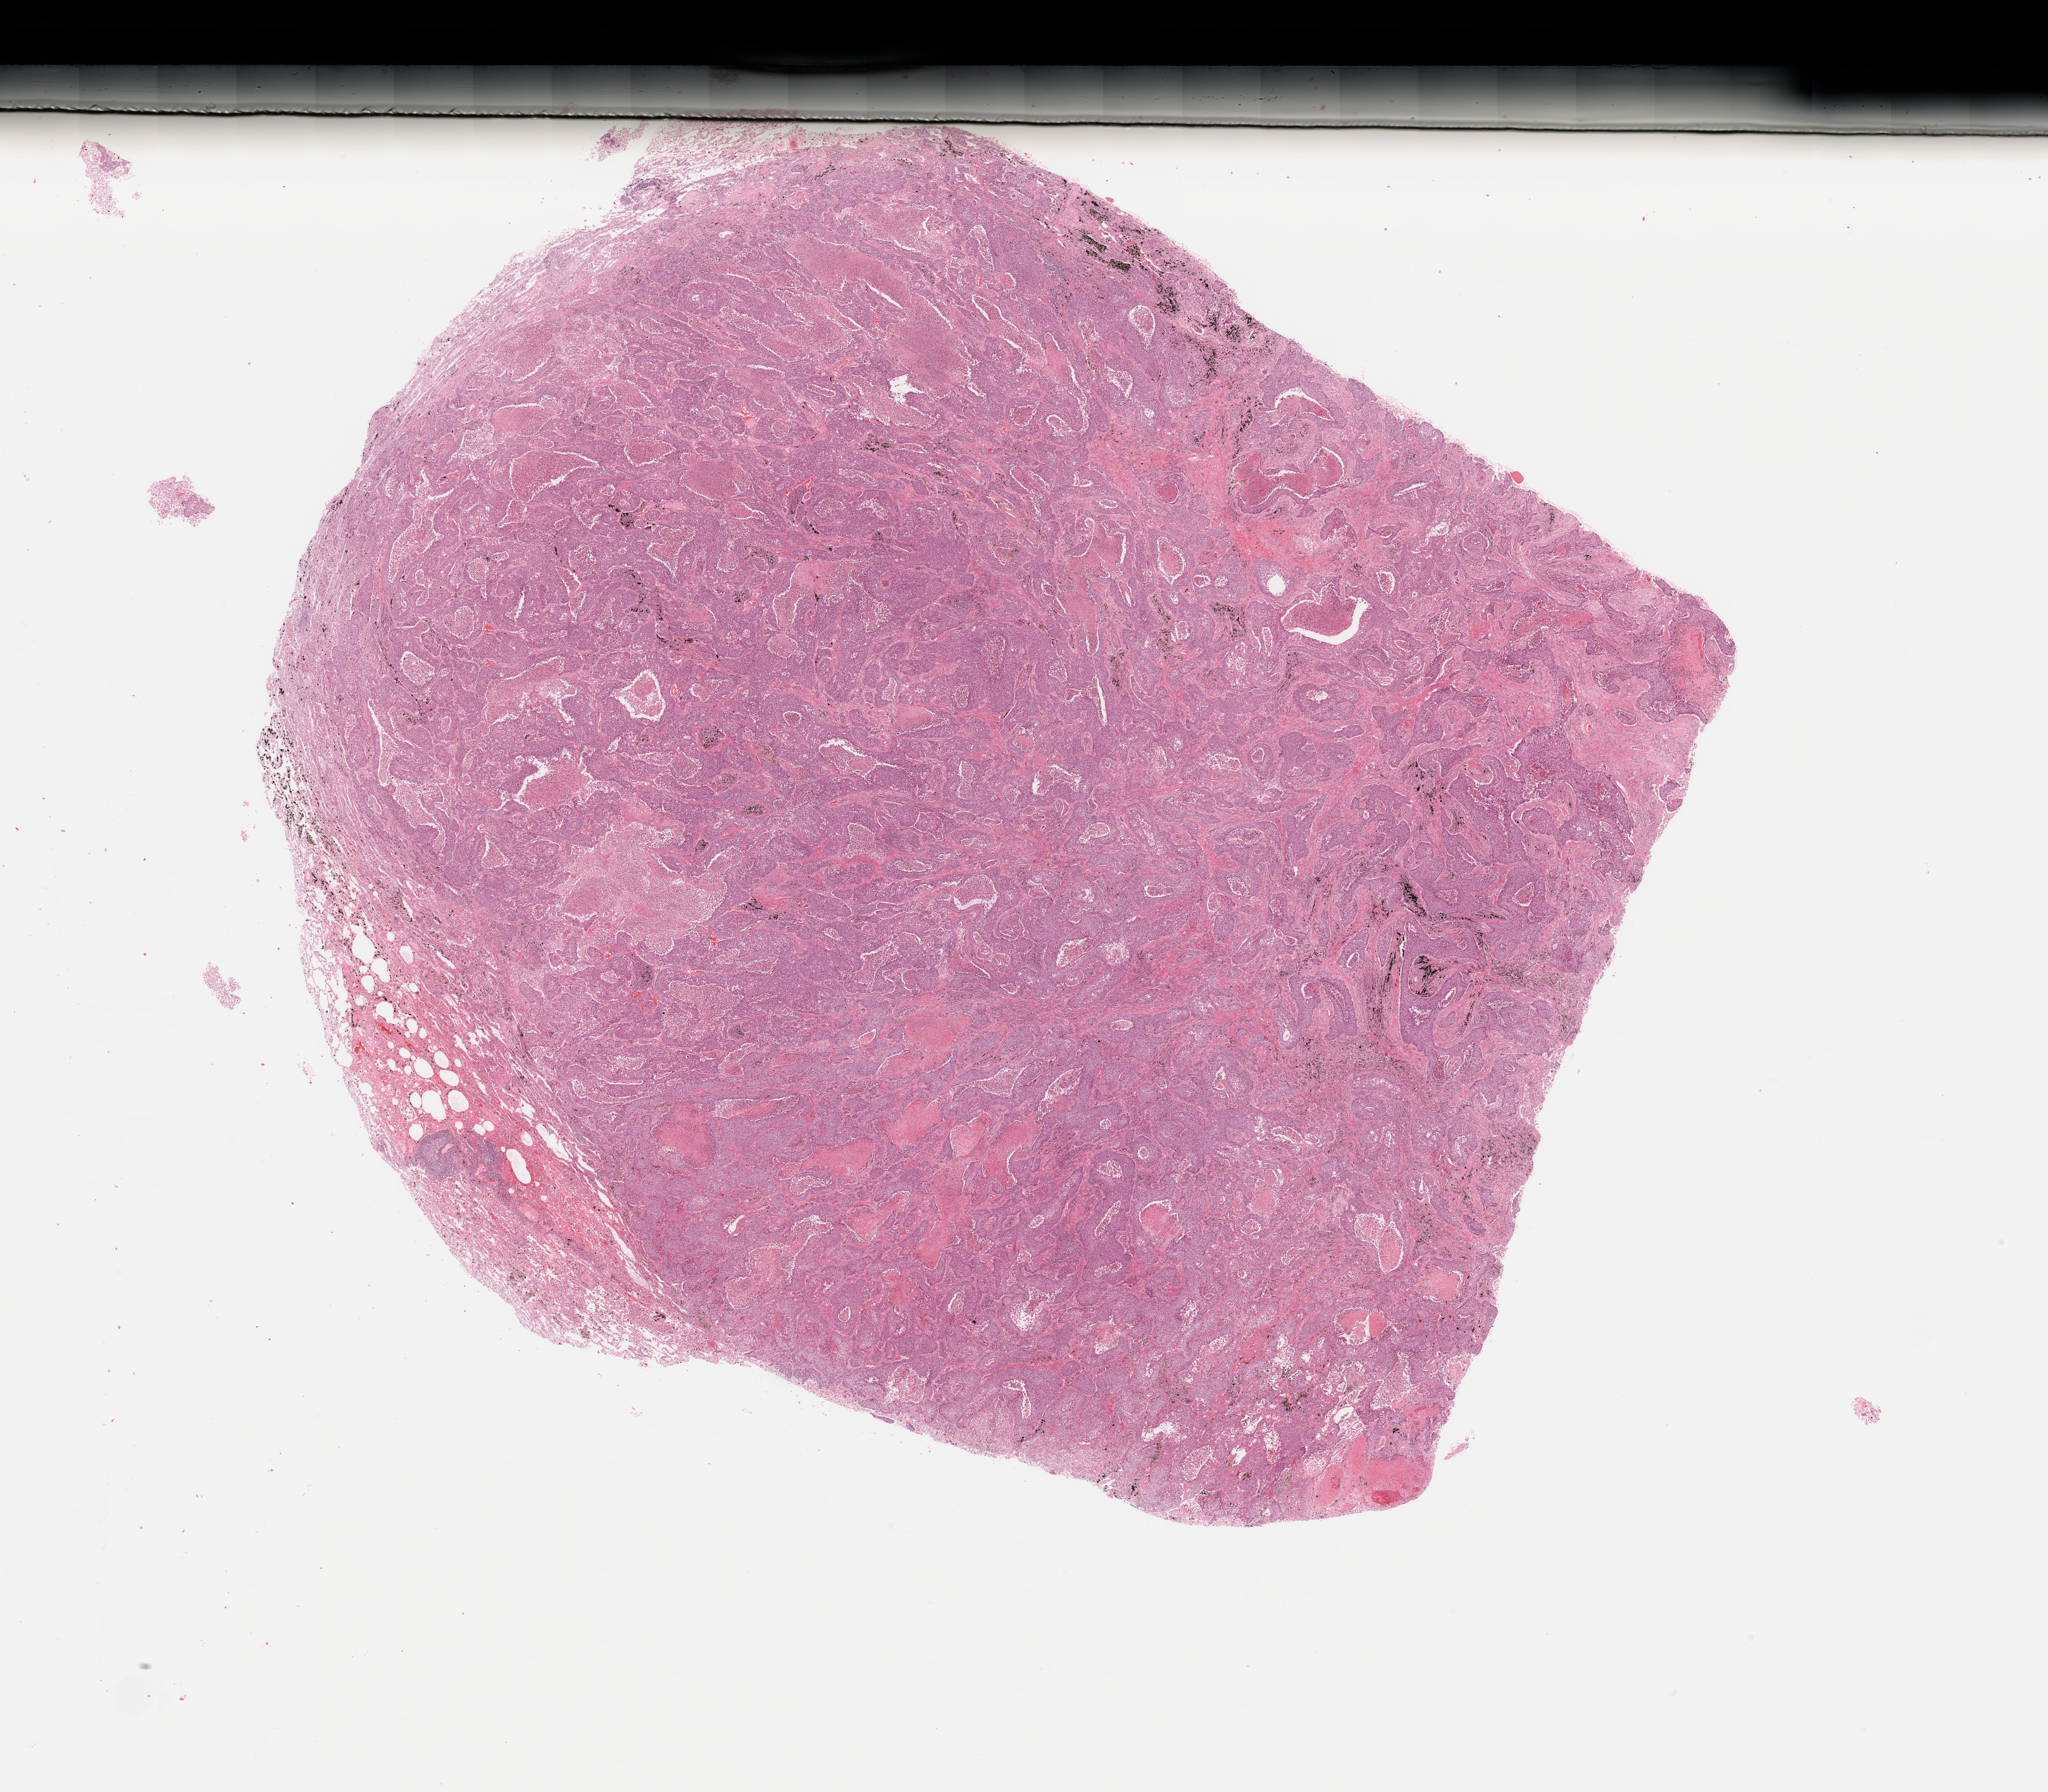
H&E whole-slide image, whole scanned area (about 25.6 x 22.4 mm) shown as a low-resolution overview, tumour tissue sample, lung. Patient: male, age 52 years. Histologic grade: G3 (poorly differentiated).
Diagnosis: Squamous cell carcinoma, NOS. AJCC pathologic stage: IIB.